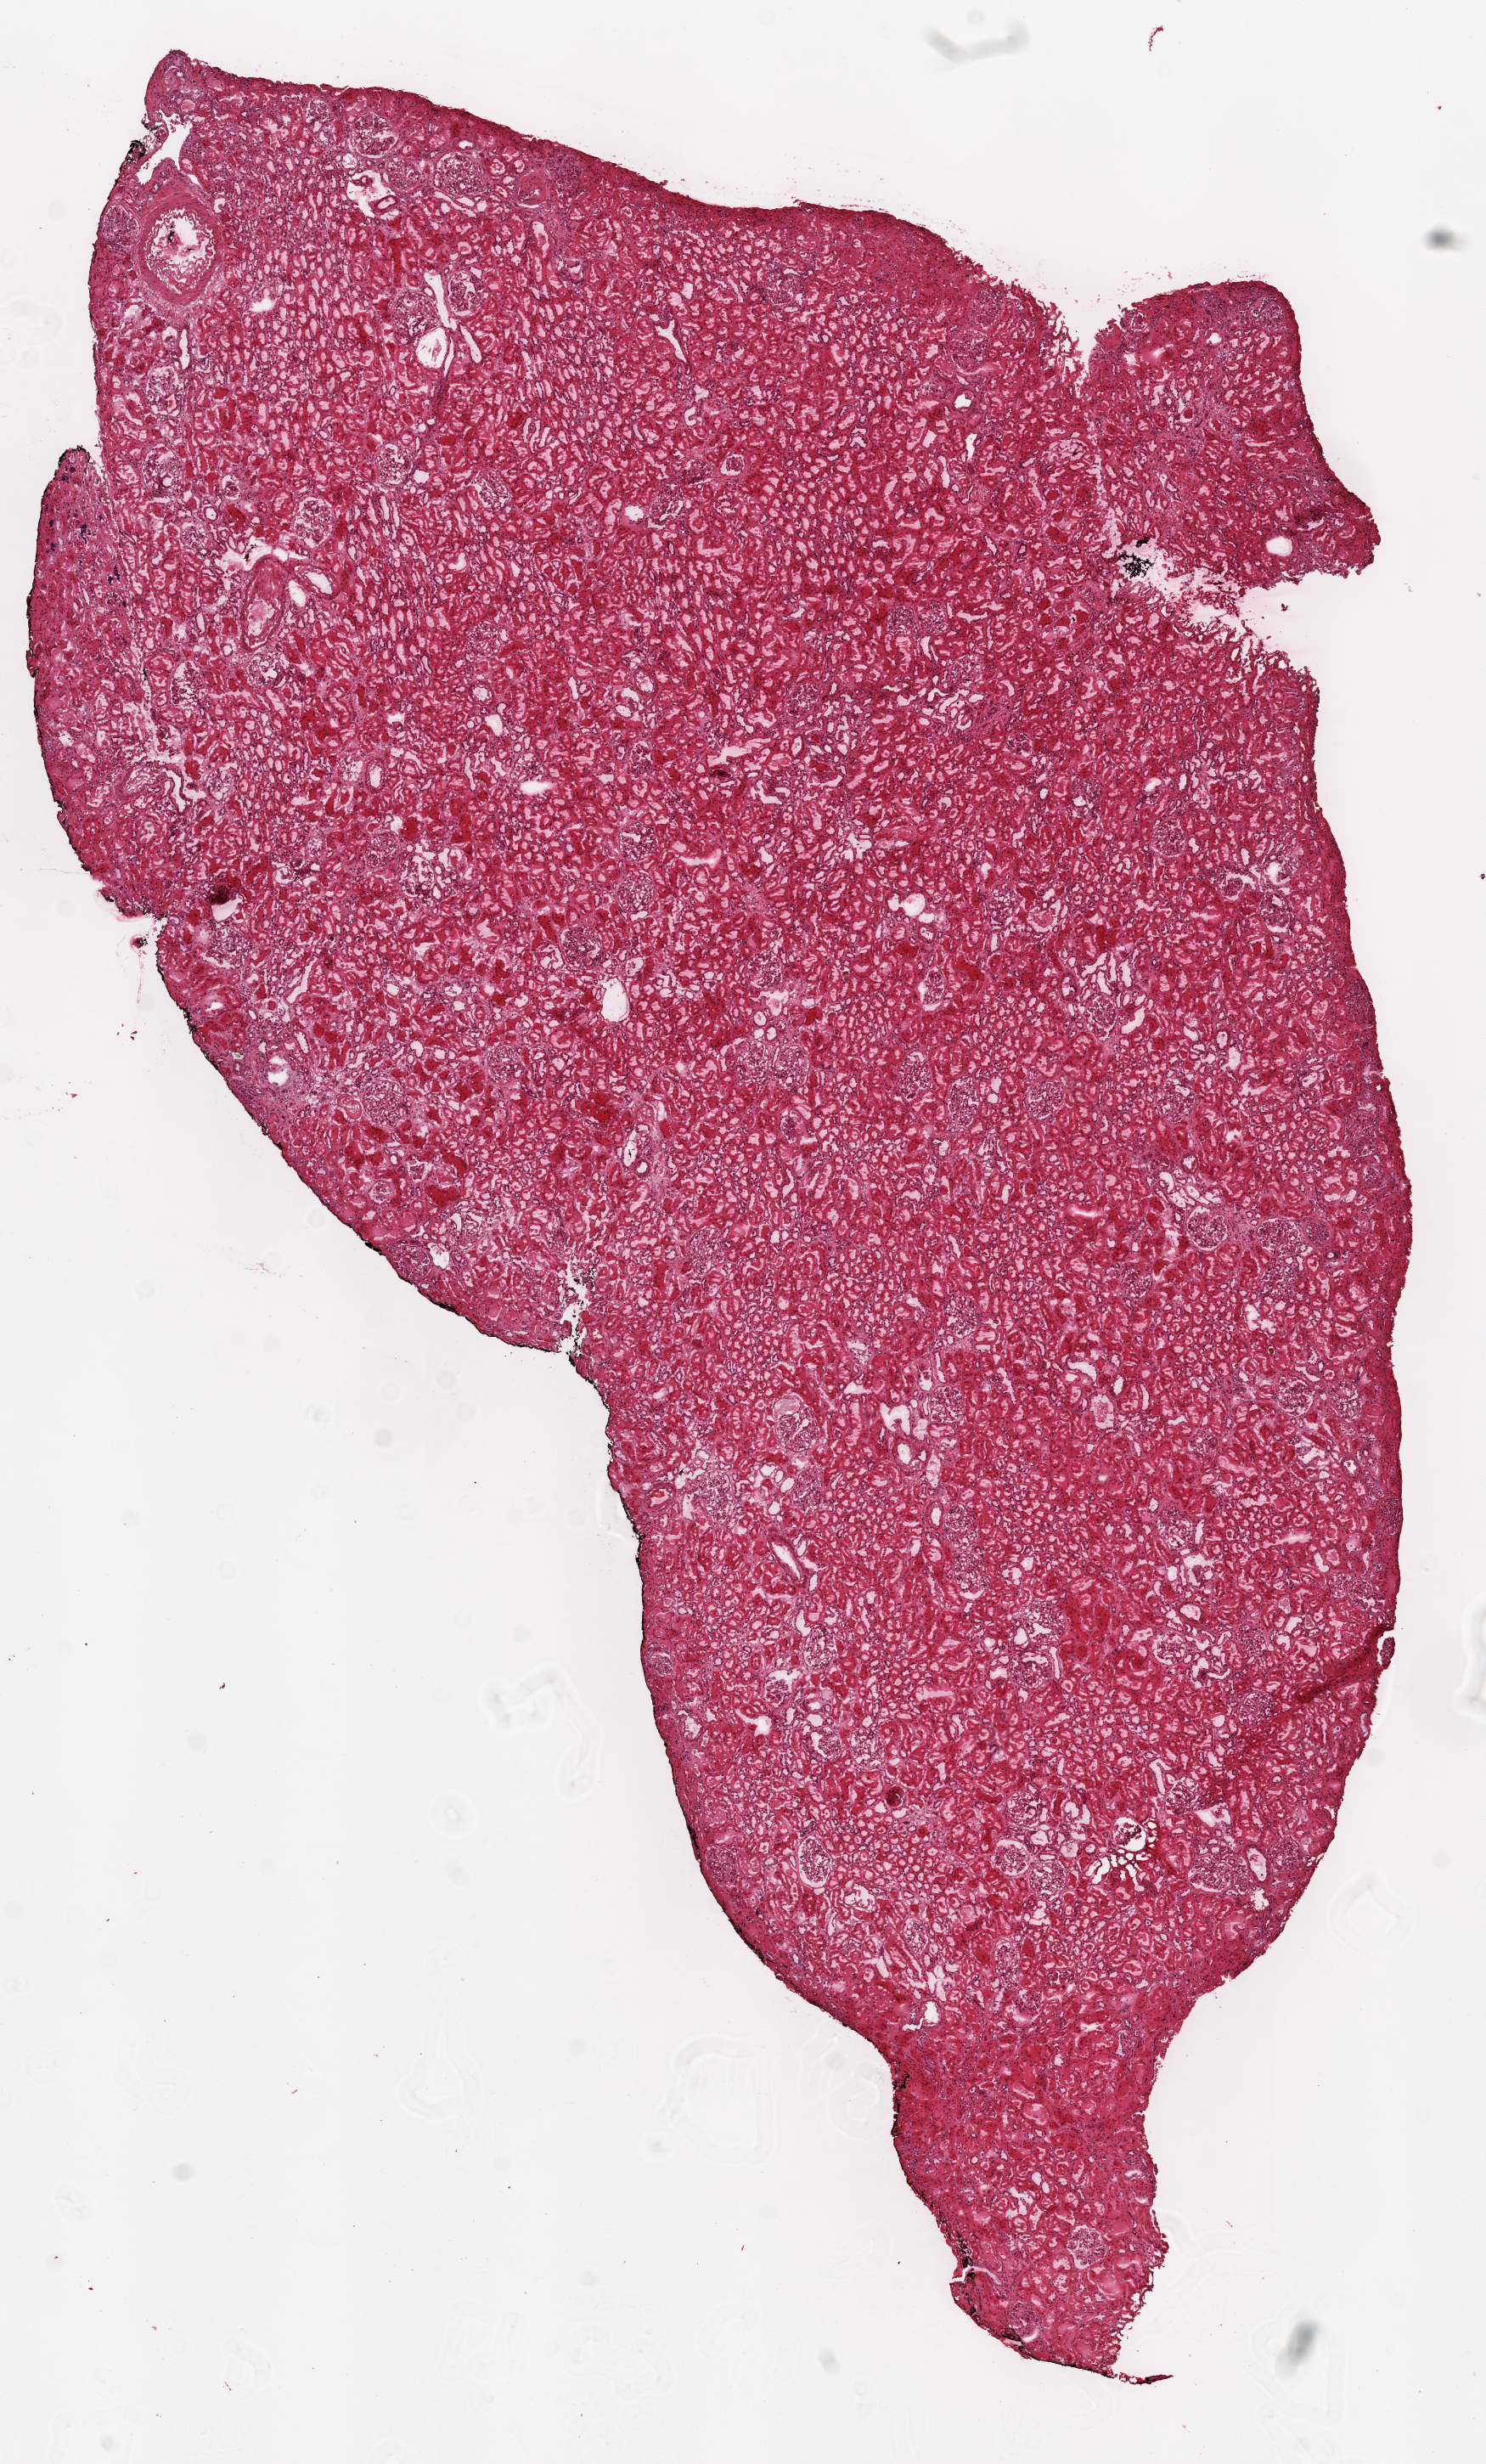
H&E-stained whole-slide image, low-resolution overview of the scanned area, about 7.0 x 11.6 mm. Frozen section. Solid tissue normal (non-tumour tissue) sample from the kidney. Patient: male, age at initial diagnosis 48 years.
This section: solid tissue normal sample (biorepository sample class). Patient diagnosis: Clear cell adenocarcinoma, NOS.